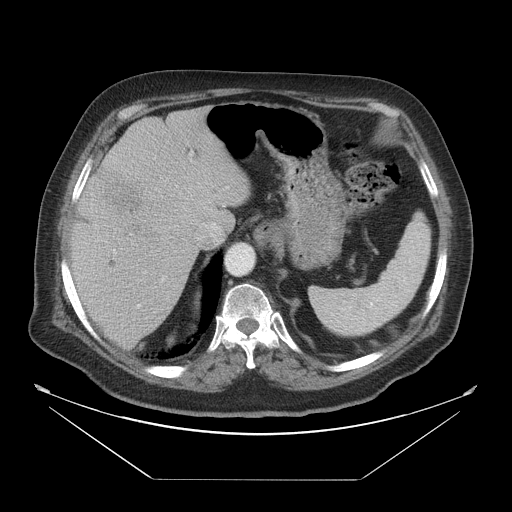
Contrast-enhanced abdominal CT, one axial slice. Slice 38 of 45 in the series (ordered by position). Reconstruction kernel STANDARD. Intravenous contrast given. Soft-tissue window (W 400 / L 40 HU). 5 mm slice thickness. 512 × 512 image matrix, field of view 463 × 463 mm. Male patient, age 87 years. From the clinical record (not read from this slice): diagnosis: colorectal cancer liver metastases, imaged before liver resection.
Structures marked on this image (manually delineated by an expert):
- hepatic veins: bounding box <171,207,188,238> (left, top, right, bottom; pixels)
- liver: <71,107,253,347>
- planned liver remnant (the part of the liver to remain after resection): <110,106,253,213>
- portal vein (with intrahepatic branches): <129,150,194,282>
- liver metastasis: <123,221,147,243>
- liver metastasis: <94,166,148,214>